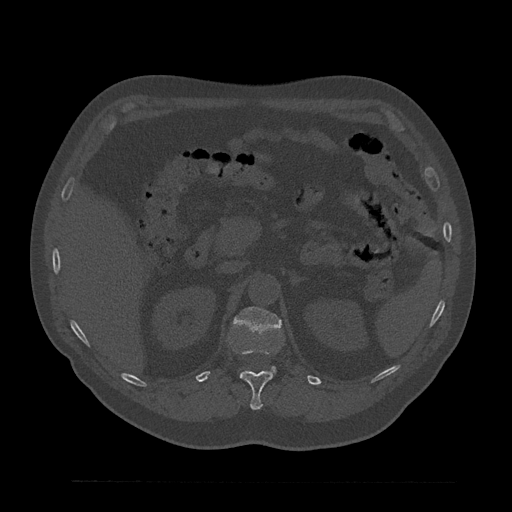
CT including the spine, one axial slice. Position 206 of 797 along the scan axis. Reconstruction kernel Br40s/3. 120 kVp. Bone window (W 1800 / L 400 HU). 0.5 mm slice thickness. 512 × 512 image matrix. Male patient, age 61 years. From the clinical record (not read from this slice): primary cancer: prostate.
Structures marked on this image (semi-automatically segmented with operator editing):
- L1 vertebra: bounding box (x1, y1, x2, y2) in pixels: (234, 307, 281, 373)
- T12 vertebra: (239, 348, 273, 410)